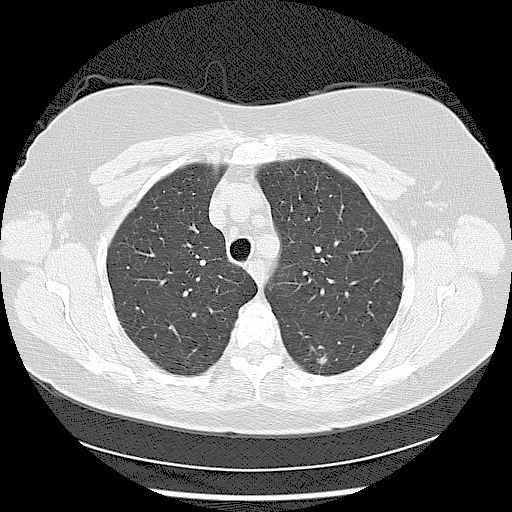
Chest CT (low-dose screening protocol), one axial image. Baseline screening round. Lung window (W 1500 / L -600 HU). 2.5 mm slice thickness. Lung (sharp) reconstruction kernel (LUNG). 120 kVp. Female, age 56 years at enrolment. Current smoker at enrolment.
Expert reader's lesion annotation, box from (x=294, y=336) to (x=344, y=388) px. The screening reader recorded 2 non-calcified nodules or masses ≥4 mm on this exam; which of them this box marks is not recorded. Official screen result: positive, change unspecified: nodule(s) >= 4 mm or enlarging nodule(s), mass(es), or other non-specific abnormalities suspicious for lung cancer. Later outcome: lung cancer diagnosed 638 days after this screen — adenocarcinoma, NOS, left lower lobe, moderately differentiated (G2), stage IIA (AJCC 6th edition), 15 mm at pathology.